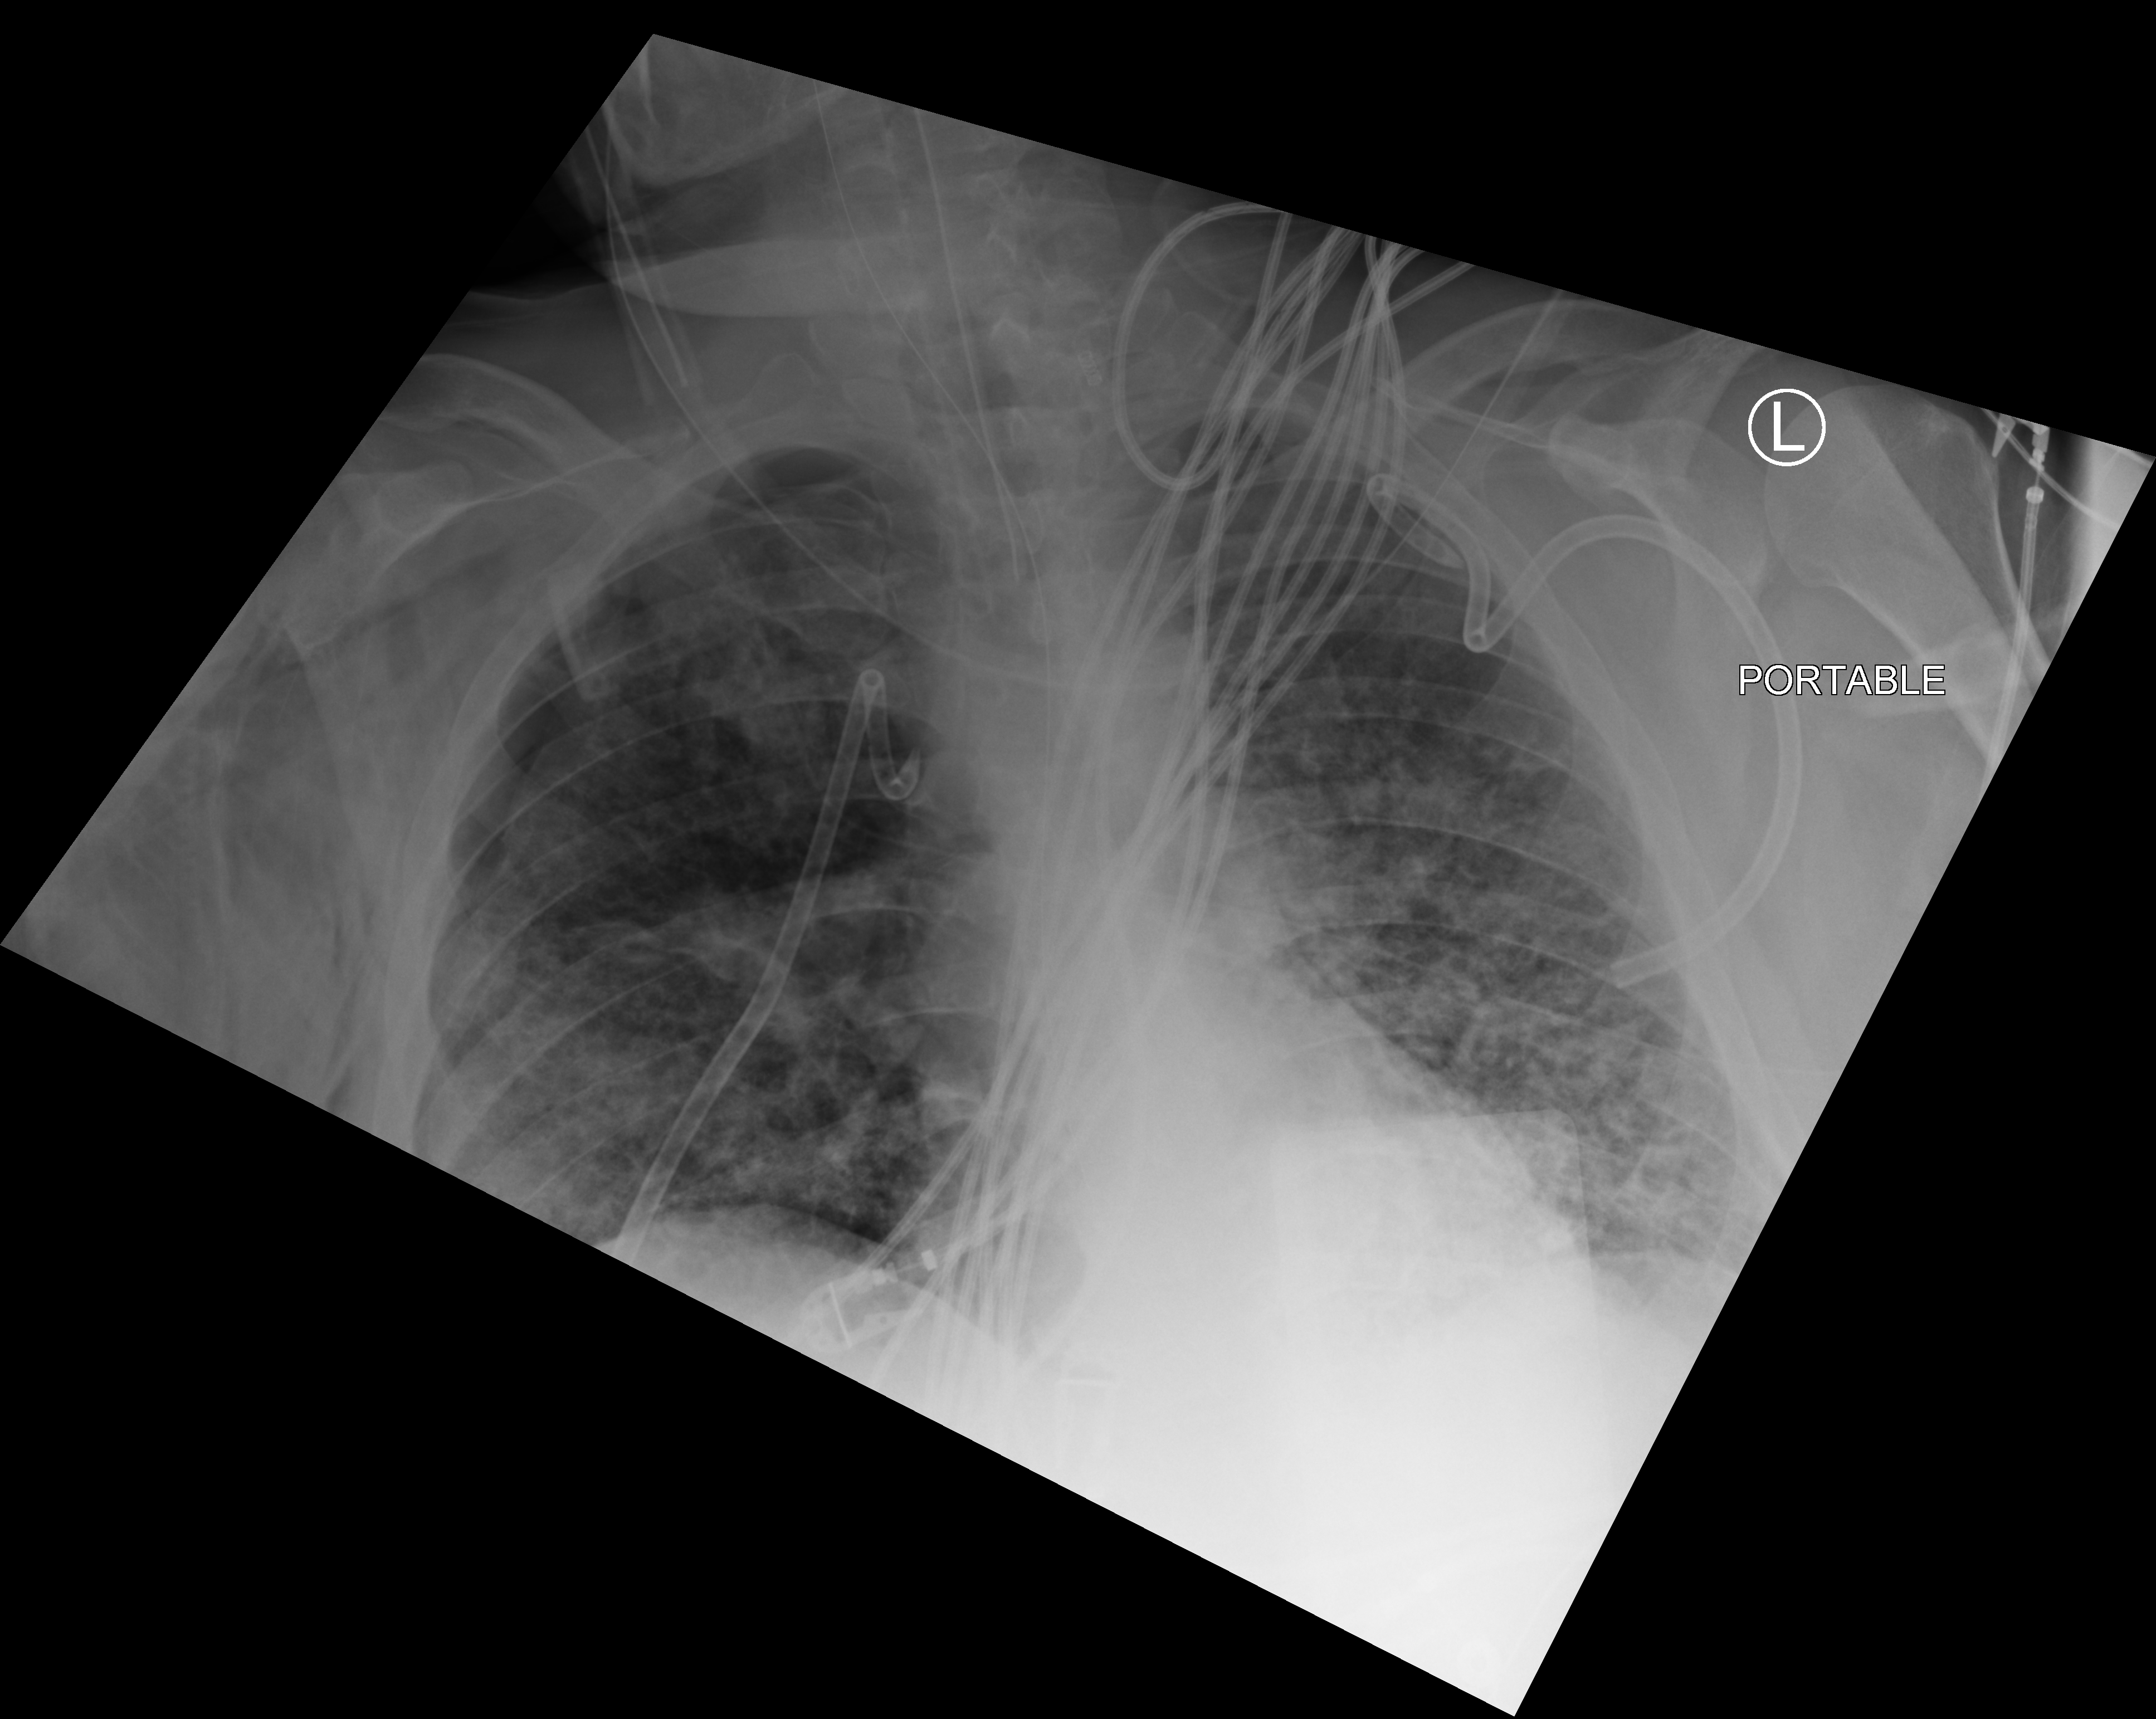
Chest X-ray (portable); anteroposterior (AP) projection. Patient hospitalised with COVID-19, aged 18–59 years.
Hospital-stay facts (about this admission, not read from this image; timing relative to this image not recorded): mechanically ventilated during this hospital stay: yes; admitted to intensive care during this hospital stay: yes.